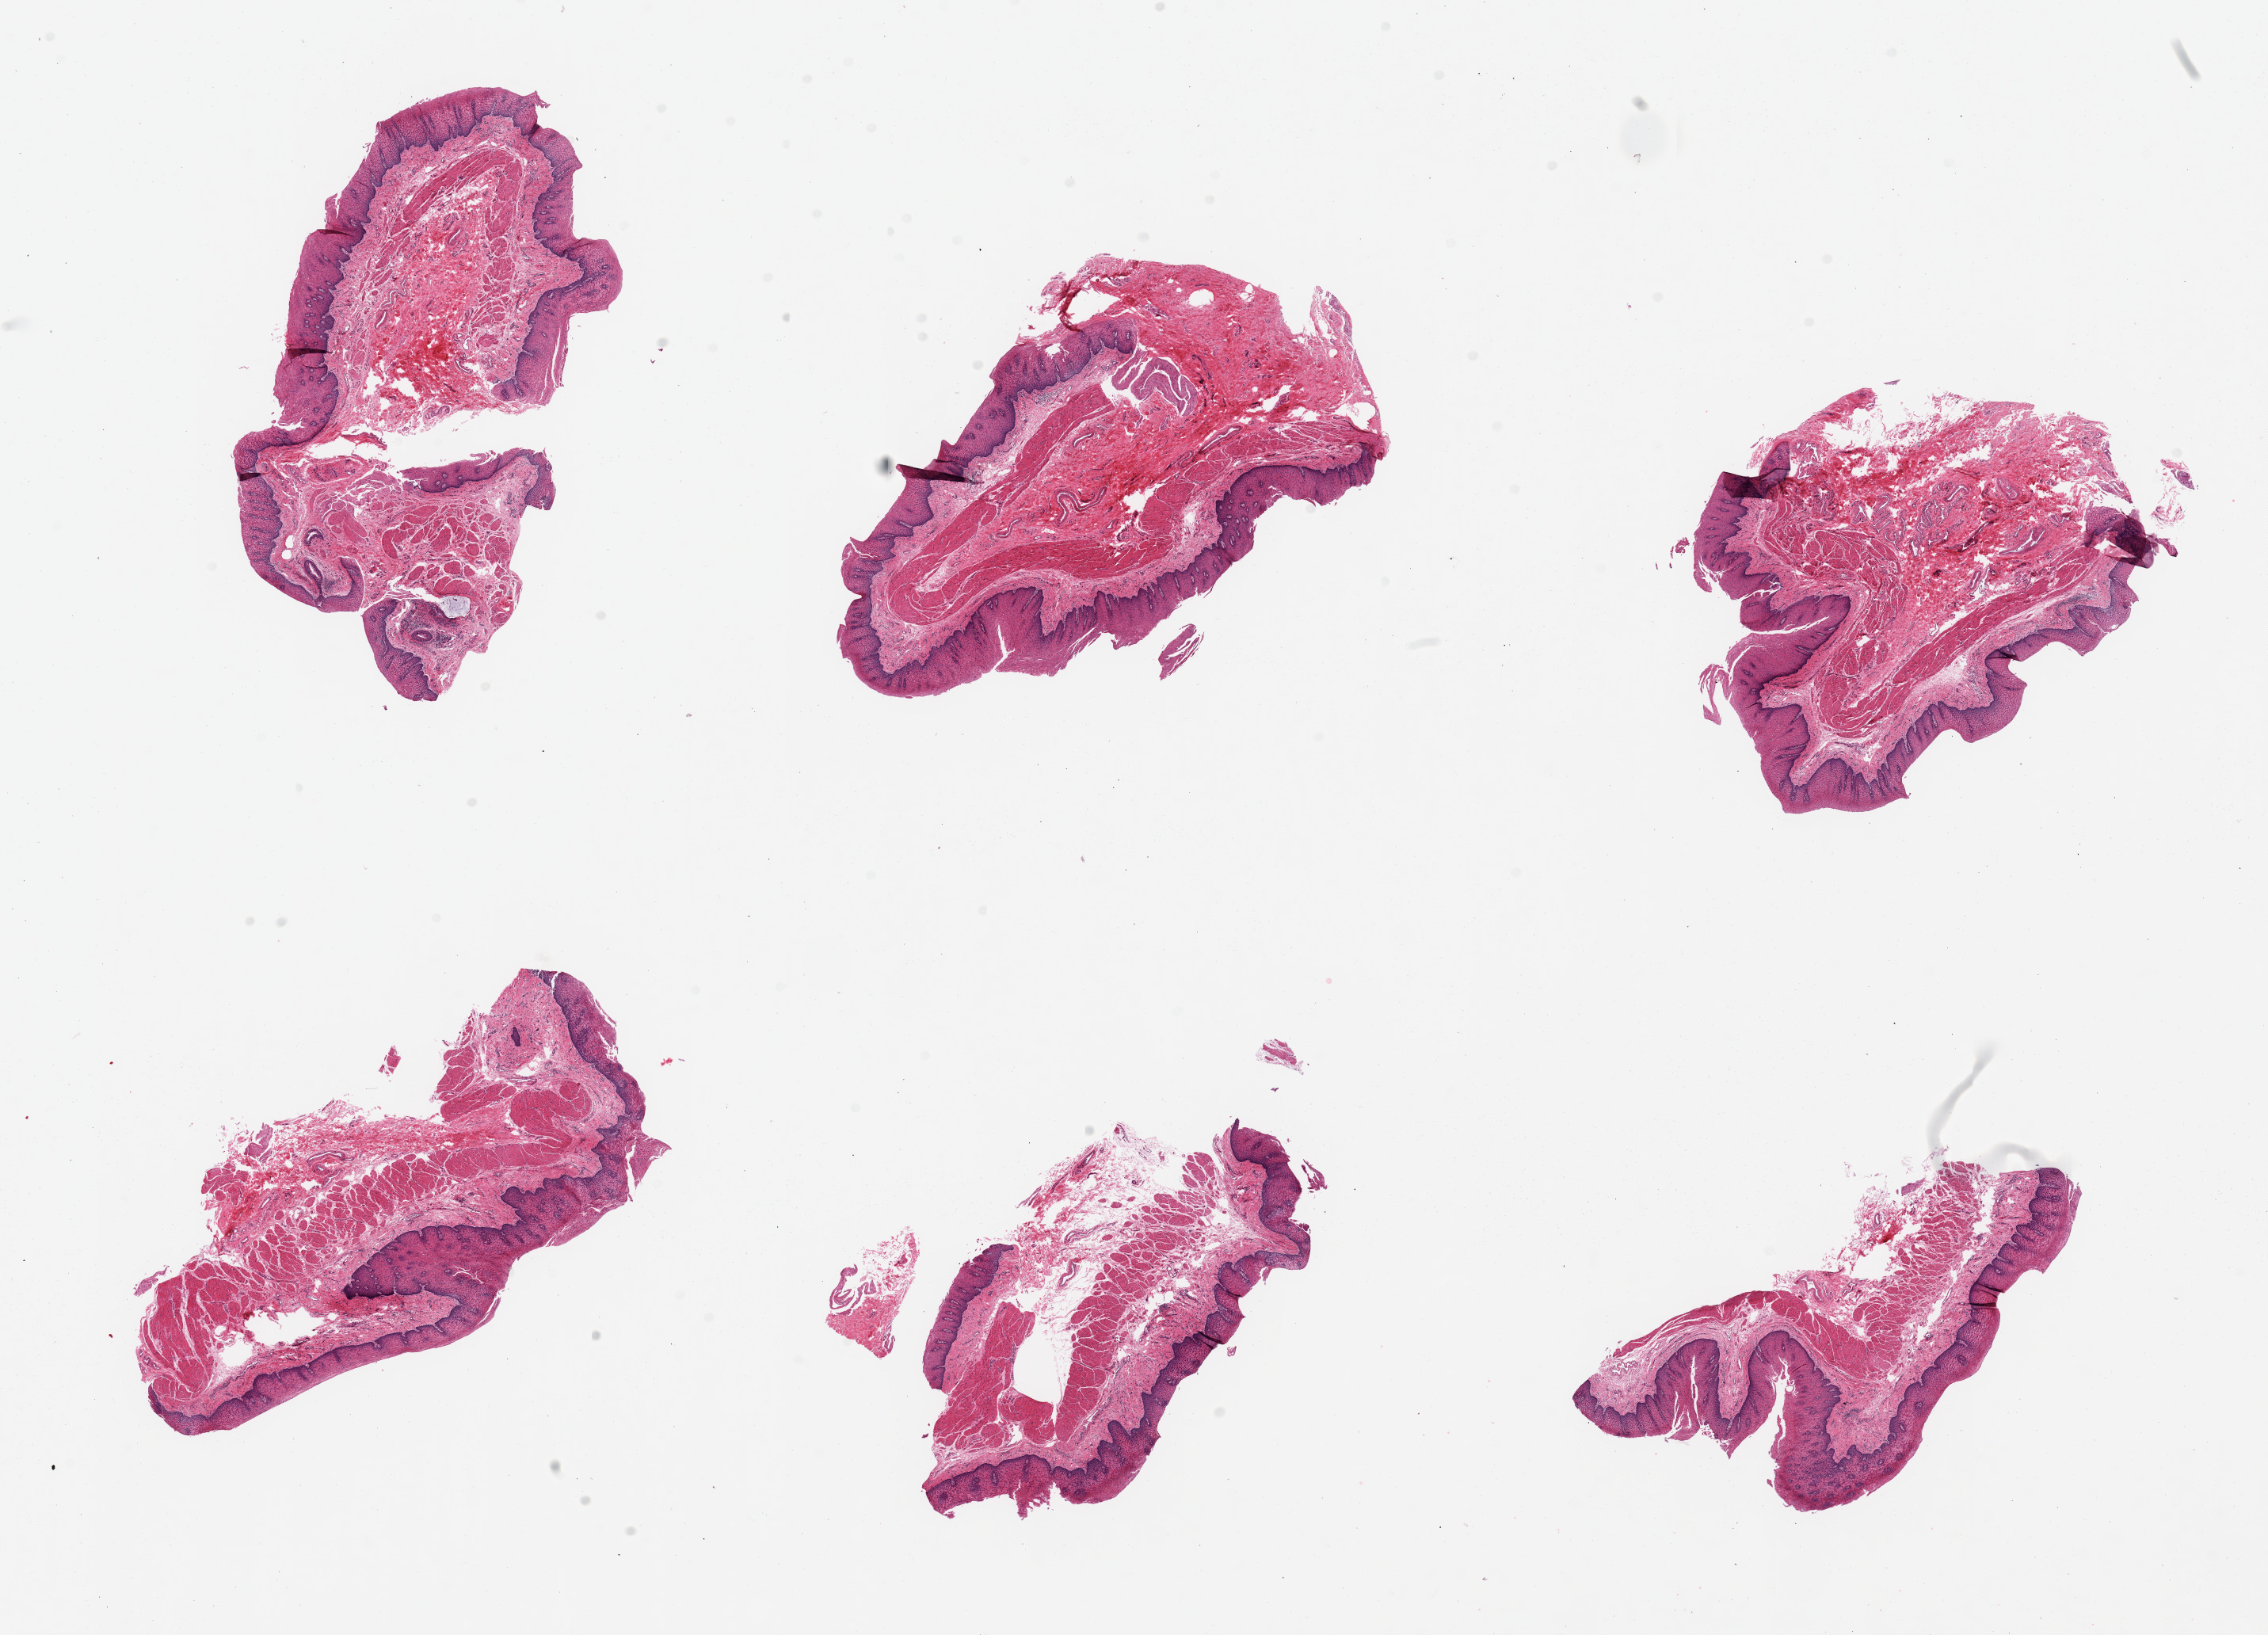
Haematoxylin and eosin whole-slide image, brightfield — shown as a low-resolution overview of the whole scanned area (about 22.6 x 16.3 mm, from a 20x scan). PAXgene-fixed paraffin-embedded (PFPE) section. Target tissue: esophageal mucous membrane. Tissue donor sample. Donor sex: female.
Pathologist's review note for this sample: 6 pieces, squamous mucosa up to ~0.4mm, ~15-20% thickness.